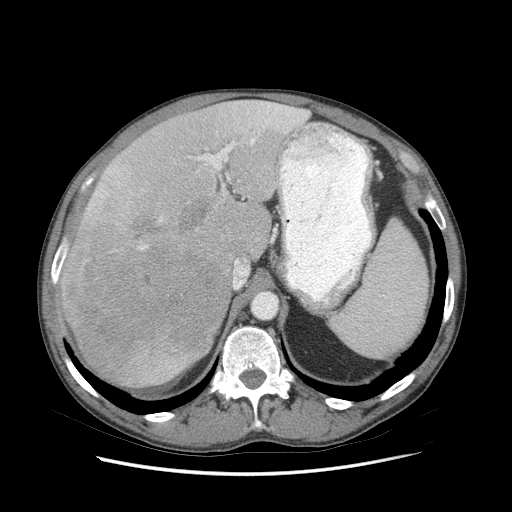
Contrast-enhanced abdominal CT (liver protocol), one axial slice. Slice 54 of 89 in the series (ordered by position). Reconstruction kernel STANDARD. Soft-tissue window (W 400 / L 40 HU). 512 × 512 image matrix, field of view 380 × 380 mm. Case-level facts recorded for this patient, not image findings: diagnosis: hepatocellular carcinoma (patient treated with transarterial chemoembolisation; whether this scan precedes or follows treatment is not stated here); TNM stage (as recorded): Stage-IIIB; Child-Pugh class: A; tumour differentiation: moderately differentiated; tumour nodularity: multinodular.
Outlined on this slice (semi-automatic segmentation, software-assisted and operator-edited):
- liver parenchyma outside the tumour (the mass and vessels are separate outlines, so this box may not span the whole liver): box from (x=58, y=100) to (x=308, y=388) px
- mass: (x=58, y=210)–(x=231, y=387)
- liver vessels: (x=59, y=102)–(x=307, y=268)